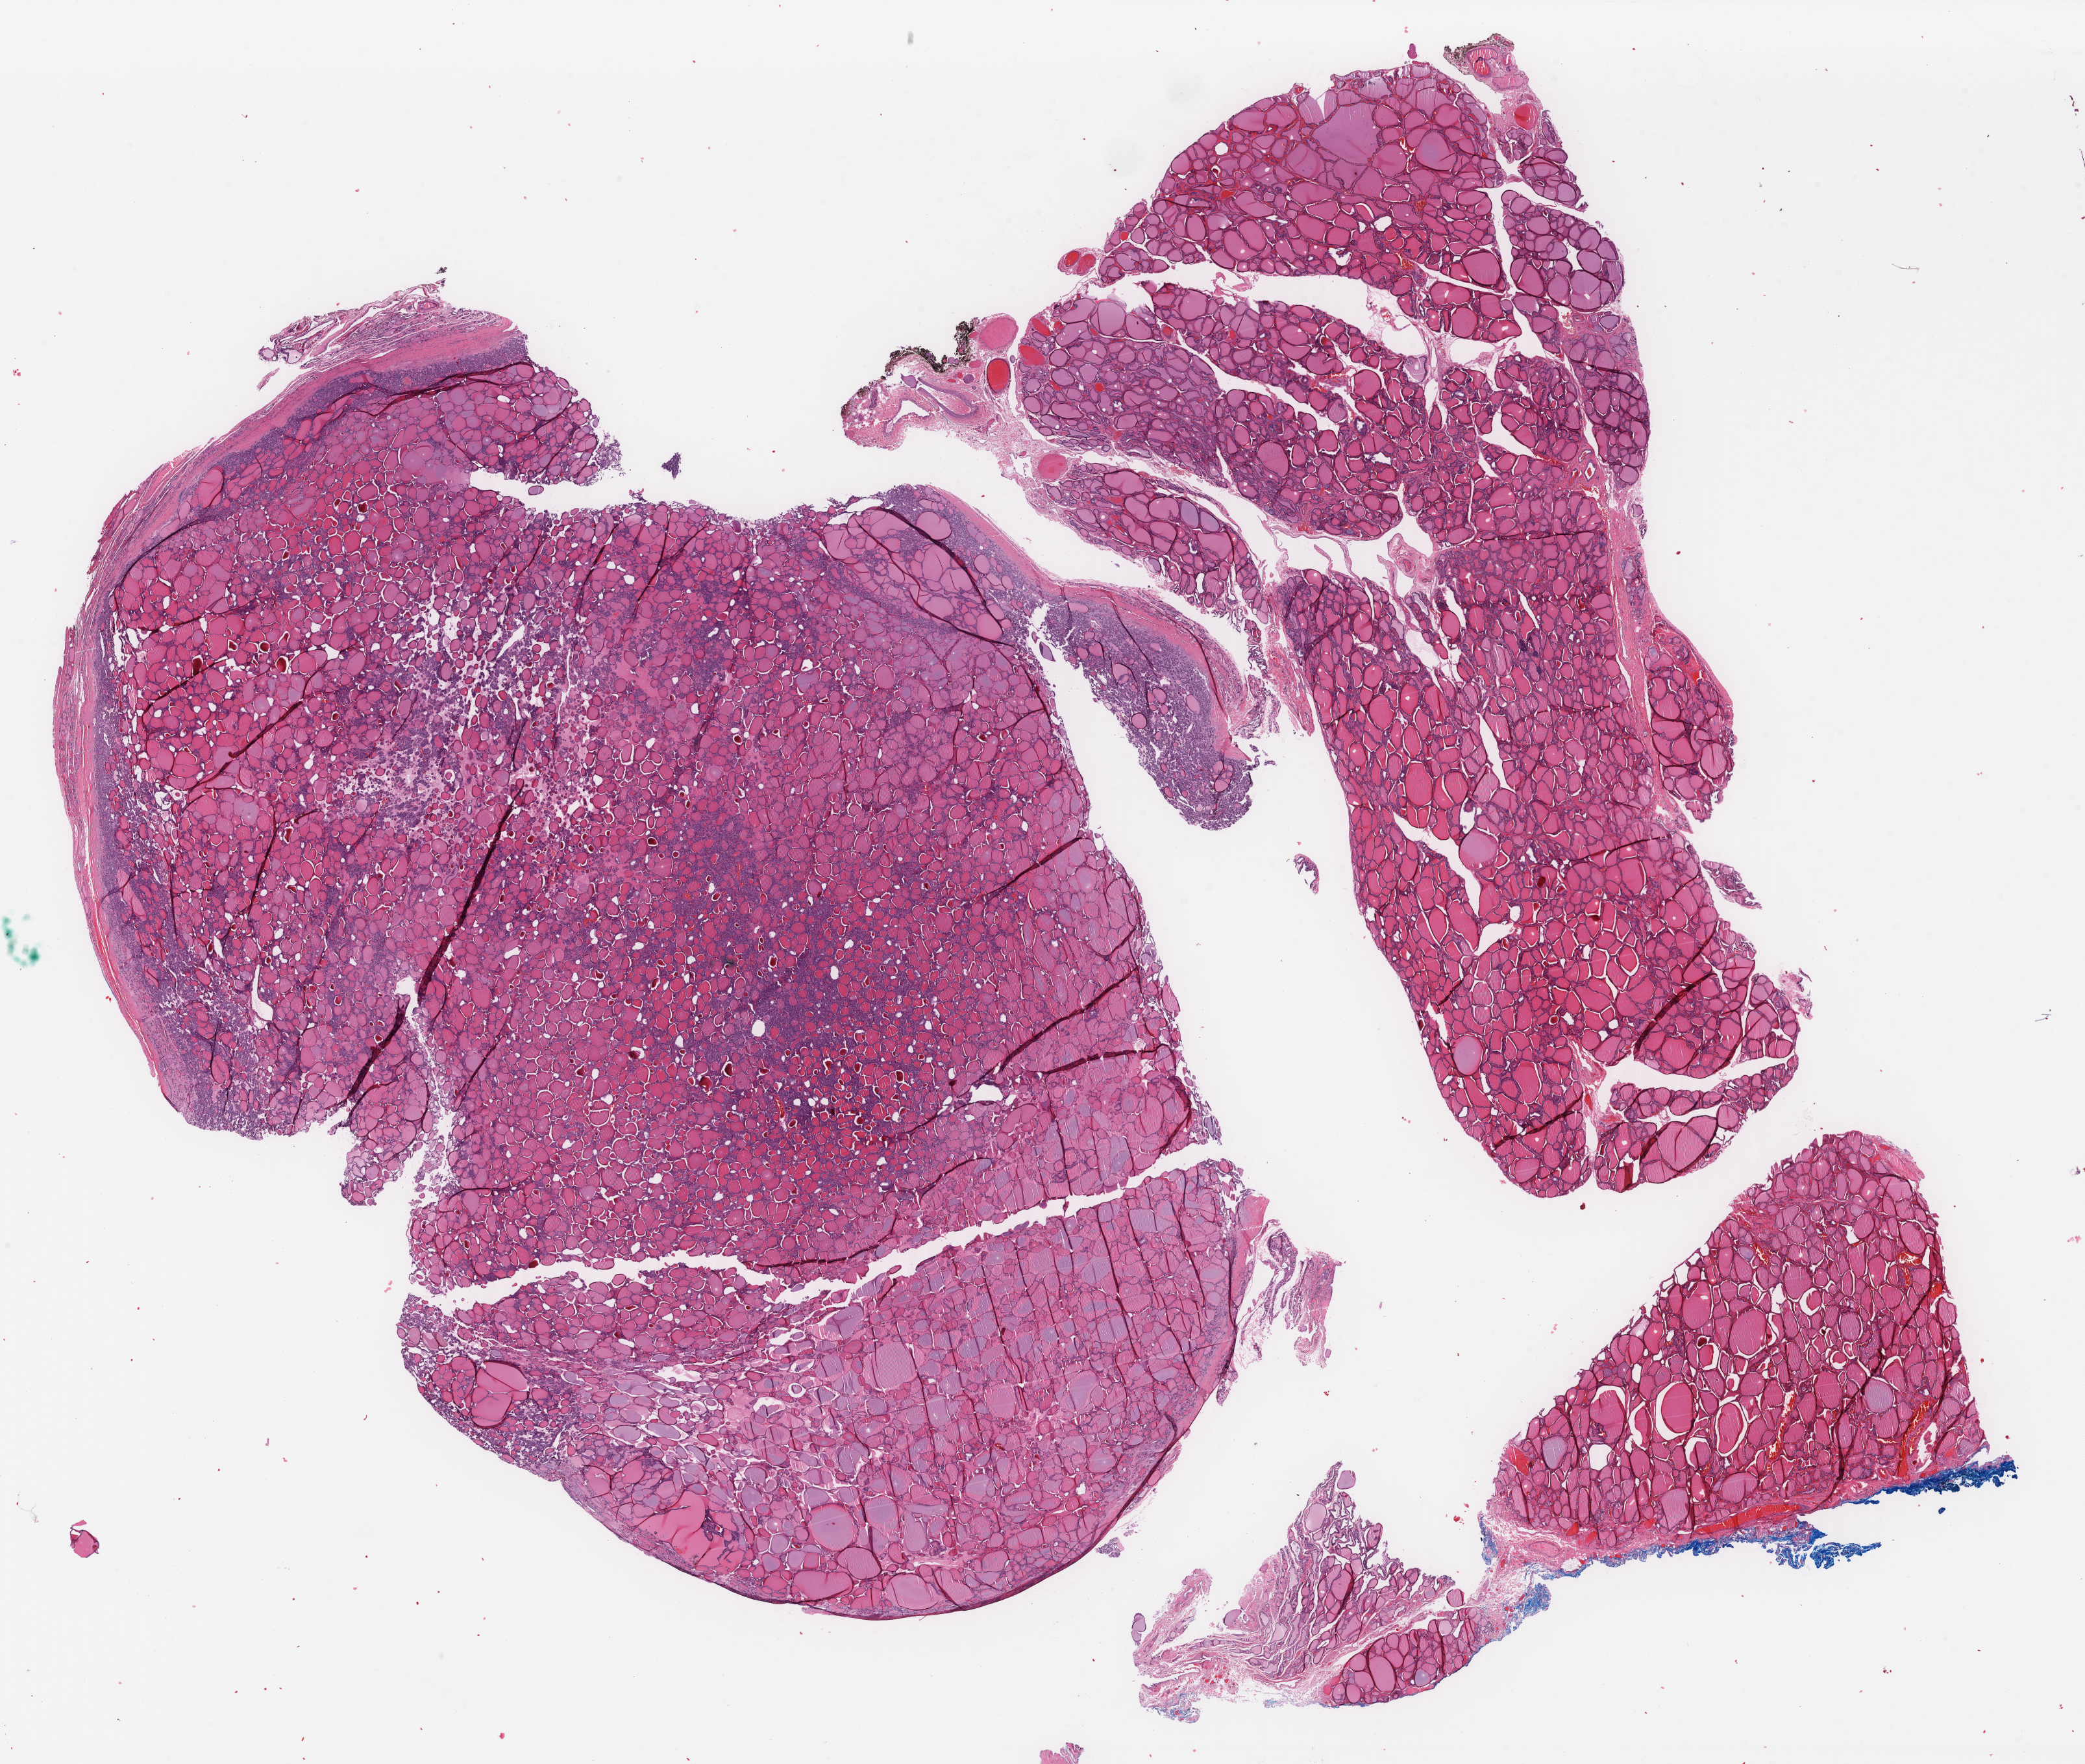
Whole-slide histology image, H&E-stained, whole scanned area (about 25.5 x 21.6 mm) shown as a low-resolution overview, FFPE section, primary tumour sample from the thyroid. Female patient; age at initial diagnosis 28 years.
• lymph nodes positive (case pathology): 0 of 5 examined
• pathologic diagnosis: Papillary carcinoma, follicular variant (thyroid gland)
• AJCC pathologic stage: I